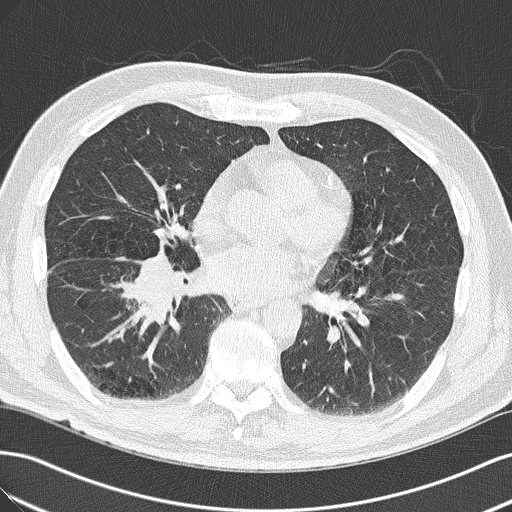
Low-dose screening chest CT, axial slice; baseline annual screen; lung window (W 1500 / L -600 HU); 2 mm slice thickness; lung (sharp) reconstruction kernel (B50f); slice 87 of 143 in the series; 512 × 512 image matrix. Male, age 65 years at enrolment. Current smoker at enrolment.
Lesion marked by an expert reader, bounding box <103,252,207,340> (left, top, right, bottom; pixels). Reader record for this screening exam (exam-level; its link to the box is not recorded): non-calcified nodule or mass ≥4 mm, right upper lobe, 18 × 13 mm, spiculated (stellate) margins, soft tissue attenuation. Official screen result: positive, change unspecified: nodule(s) >= 4 mm or enlarging nodule(s), mass(es), or other non-specific abnormalities suspicious for lung cancer. Later outcome: lung cancer diagnosed 14 days after this screen — adenocarcinoma, NOS, right lower lobe, poorly differentiated (G3), stage IIIA (AJCC 6th edition), 40 mm at pathology.